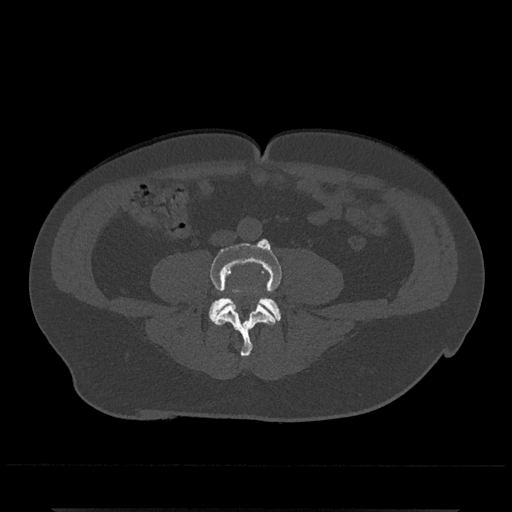
CT including the spine, one axial slice. Position 131 of 797 along the scan axis. Reconstruction kernel Br40s/3. Bone window (W 1800 / L 400 HU). 0.5 mm slice thickness. 512 × 512 image matrix, field of view 393 × 393 mm. Male patient, age 67 years. Case-level facts recorded for this patient, not image findings: primary cancer: prostate.
Structures marked on this image (semi-automatic segmentation, software-assisted and operator-edited):
- L4 vertebra: bounding box (x1, y1, x2, y2) in pixels: (210, 239, 282, 357)
- L5 vertebra: (208, 297, 281, 321)